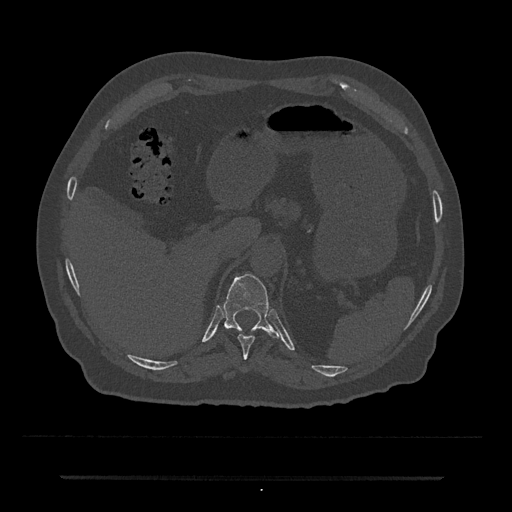
CT including the spine, one axial slice. Position 198 of 797 along the scan axis. Reconstruction kernel Br40s/3. 120 kVp. Bone window (W 1800 / L 400 HU). 0.5 mm slice thickness. 512 × 512 image matrix, field of view 437 × 437 mm. Male patient, age 69 years. From the clinical record (not read from this slice): primary cancer: prostate.
Outlined on this slice (semi-automatic segmentation, software-assisted and operator-edited):
- T10 vertebra: bounding box [x1, y1, x2, y2] px = [237, 335, 256, 359]
- T11 vertebra: [223, 273, 281, 339]